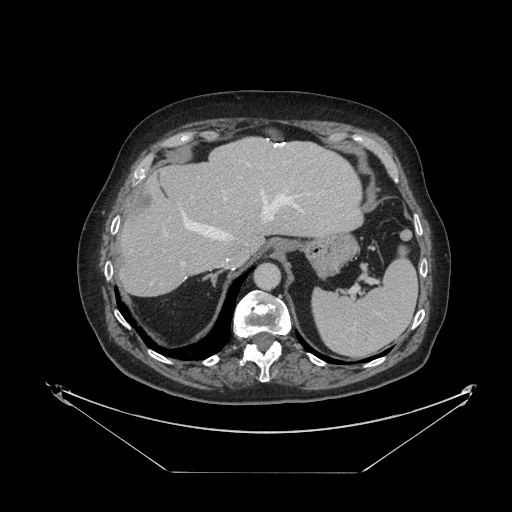
Contrast-enhanced abdominal CT, one axial slice; slice 82 of 121 in the series (ordered by position); intravenous contrast given; soft-tissue window (W 400 / L 40 HU); 2.5 mm slice thickness; 512 × 512 image matrix, field of view 500 × 500 mm. Male patient, age 68 years. Case-level facts recorded for this patient, not image findings: diagnosis: colorectal cancer liver metastases, imaged before liver resection; multiple liver metastases: no; largest metastasis: 4 cm; disease in both lobes: no.
Annotated regions visible in this slice (outlined manually by an expert reader):
- hepatic veins: bounding box [x1, y1, x2, y2] px = [182, 164, 305, 239]
- liver: [120, 138, 362, 295]
- planned liver remnant (the part of the liver to remain after resection): [120, 138, 362, 295]
- portal vein (with intrahepatic branches): [165, 191, 227, 265]
- liver metastasis: [134, 192, 154, 216]